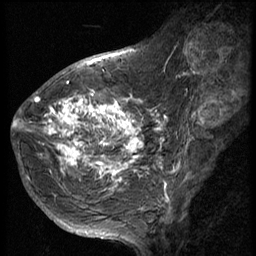
Breast MRI (dynamic contrast-enhanced), one sagittal slice. Position 21 of 56 along the scan axis. 3 images stored at this slice position (order not interpretable as contrast timing). 1.5 T. TE 4.2 ms, TR 9 ms. 256 × 256 image matrix, field of view 180 × 180 mm. Patient: female, 49 years. Case-level facts recorded for this patient, not image findings: setting: breast cancer imaged before/during neoadjuvant chemotherapy; receptor status: HER2-positive.
Structures marked on this image (semi-automatic segmentation, software-assisted and operator-edited):
- analysis volume of interest (the breast-tissue region the enhancement analysis was run in; not a lesion): bounding box (x1, y1, x2, y2) in pixels: (37, 85, 144, 207)
- tumour enhancement mask (voxels above the 140 % enhancement threshold inside the analysis volume of interest): (37, 93, 143, 205)